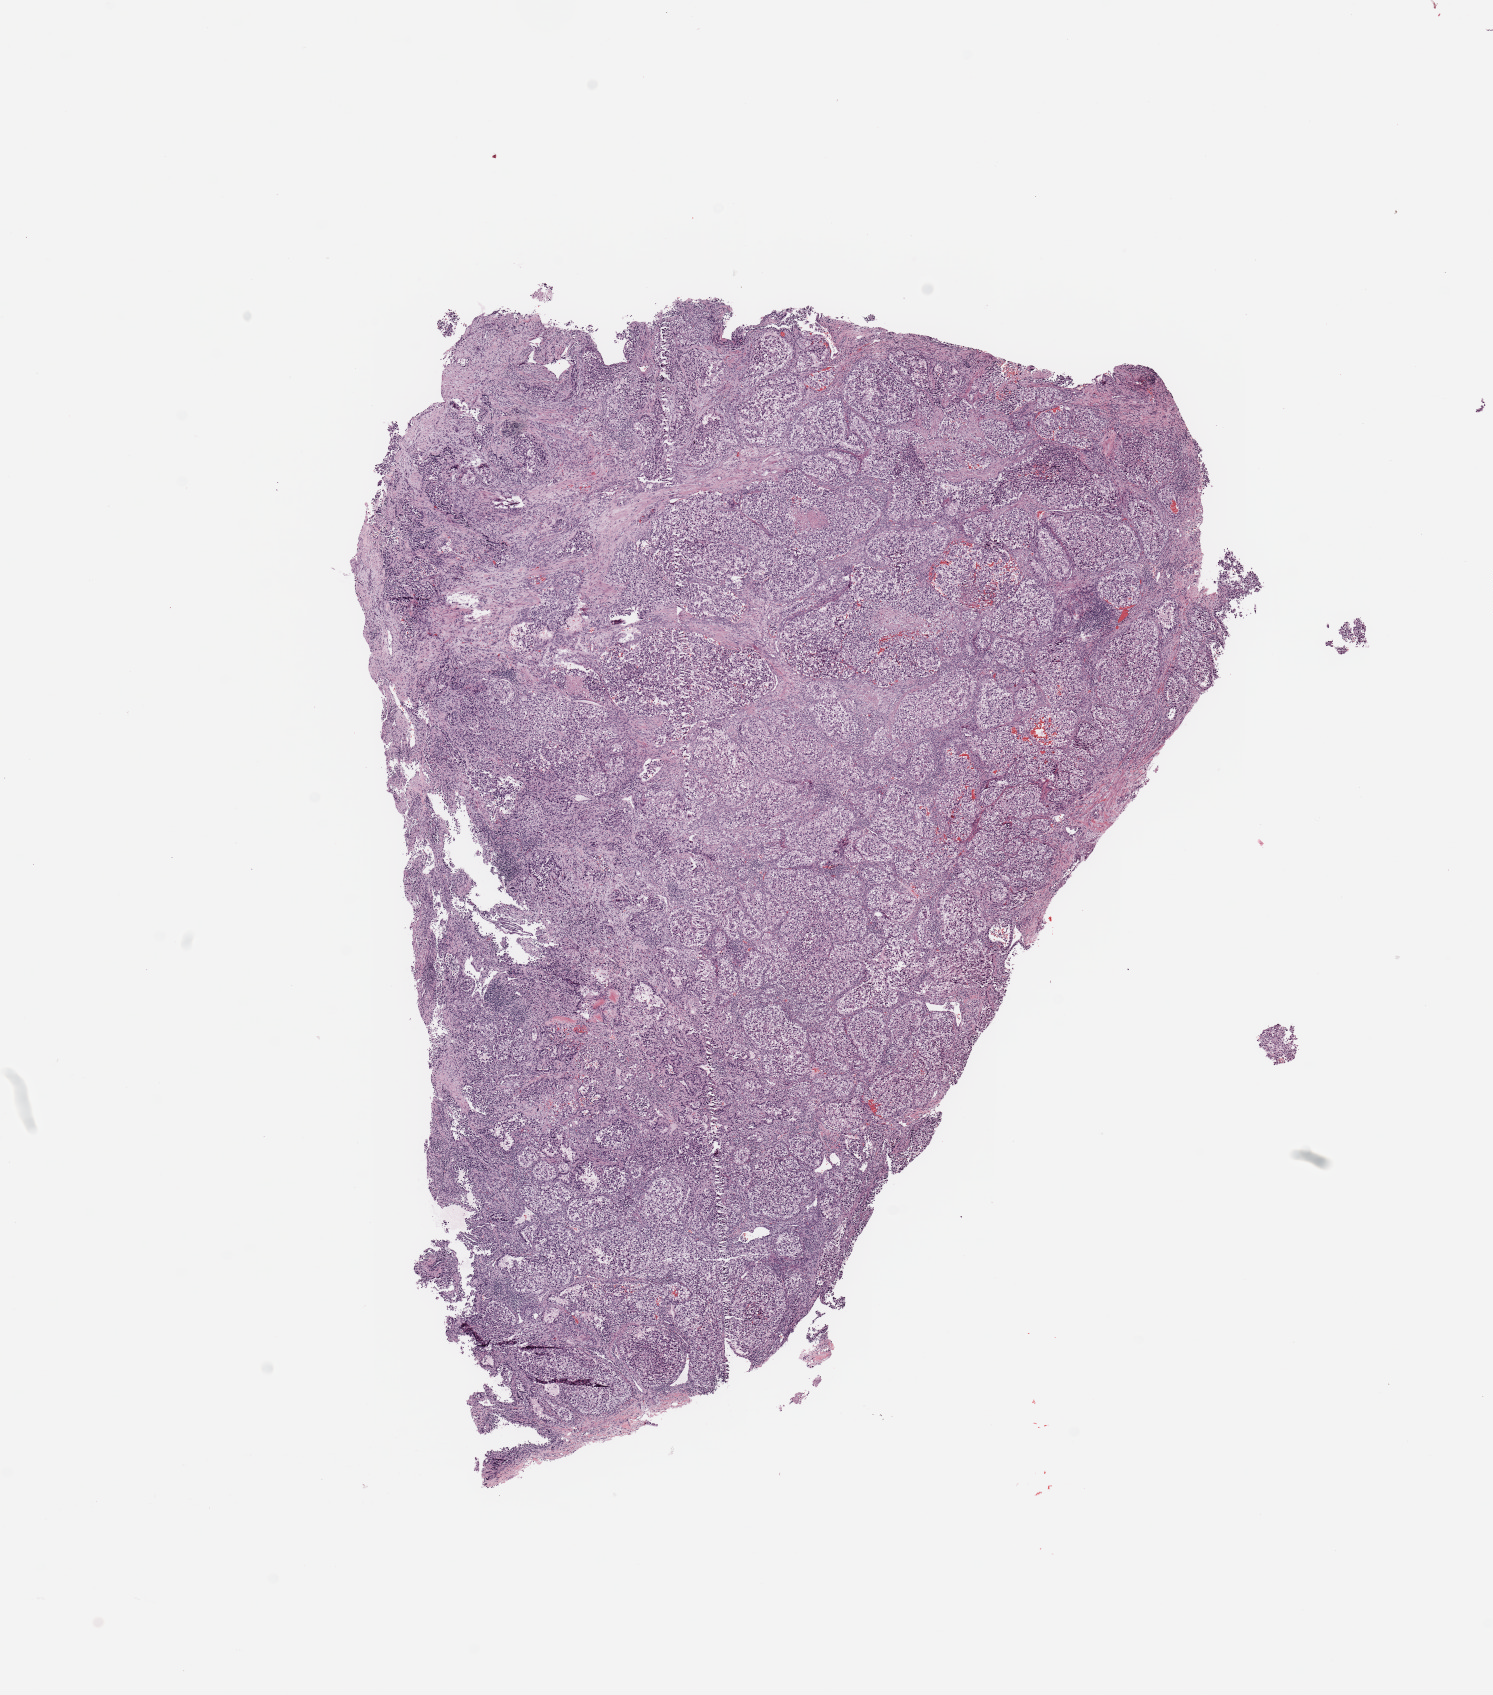
Digitized H&E tissue section (whole slide) — low-resolution overview of the scanned area, about 11.8 x 13.4 mm. Tumour tissue sample, sampled site: kidney. Male, 78 y/o. Histologic grade: G4 (undifferentiated). Slide review estimates, as recorded: tumour nuclei 90%, necrosis 2%.
Histologic diagnosis: Renal cell carcinoma, NOS. AJCC pathologic stage: III.